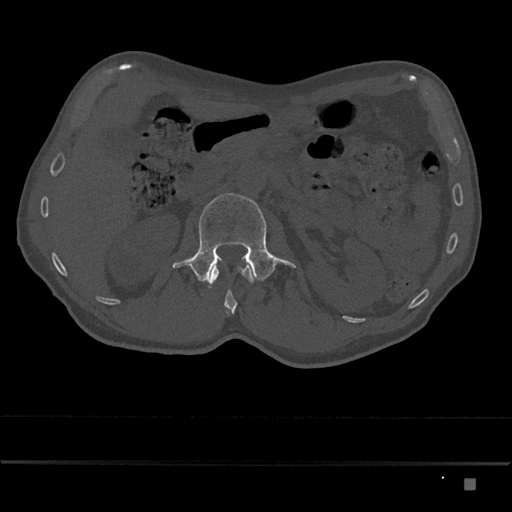
CT including the spine, one axial slice. Position 497 of 797 along the scan axis. Reconstruction kernel Br40s/3. 120 kVp. Bone window (W 1800 / L 400 HU). 0.5 mm slice thickness. 512 × 512 image matrix. Patient: male, 72 years. Case-level facts recorded for this patient, not image findings: primary cancer: prostate.
Outlined on this slice (semi-automatically segmented with operator editing):
- L1 vertebra: bounding box (x1, y1, x2, y2) in pixels: (208, 258, 254, 316)
- L2 vertebra: (172, 193, 296, 283)